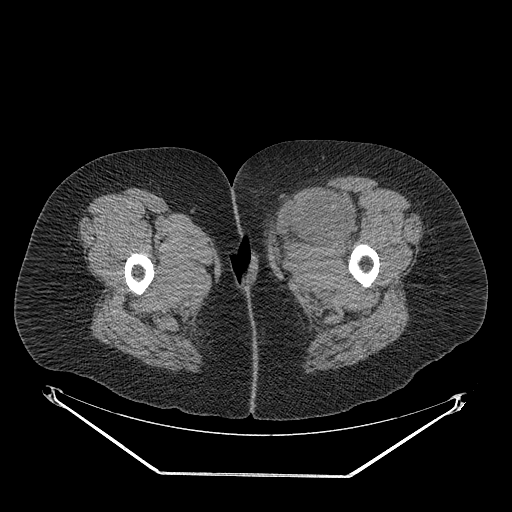
CT of an extremity soft-tissue mass (from a PET/CT study), one axial slice; slice 36 of 267 in the series (ordered by position); 140 kVp; soft-tissue window (W 400 / L 40 HU); 3.75 mm slice thickness; 512 × 512 image matrix, field of view 500 × 500 mm. Female patient. Case-level facts recorded for this patient, not image findings: histological type: myxofibrosarcoma; grade: intermediate; site of the primary tumour: left thigh.
Annotated regions visible in this slice (expert contour drawn on MRI and transferred to this co-registered scan by the dataset authors):
- gross tumour volume including surrounding oedema: bounding box <267,189,359,259> (left, top, right, bottom; pixels)
- gross tumour volume (mass): <272,189,352,243>